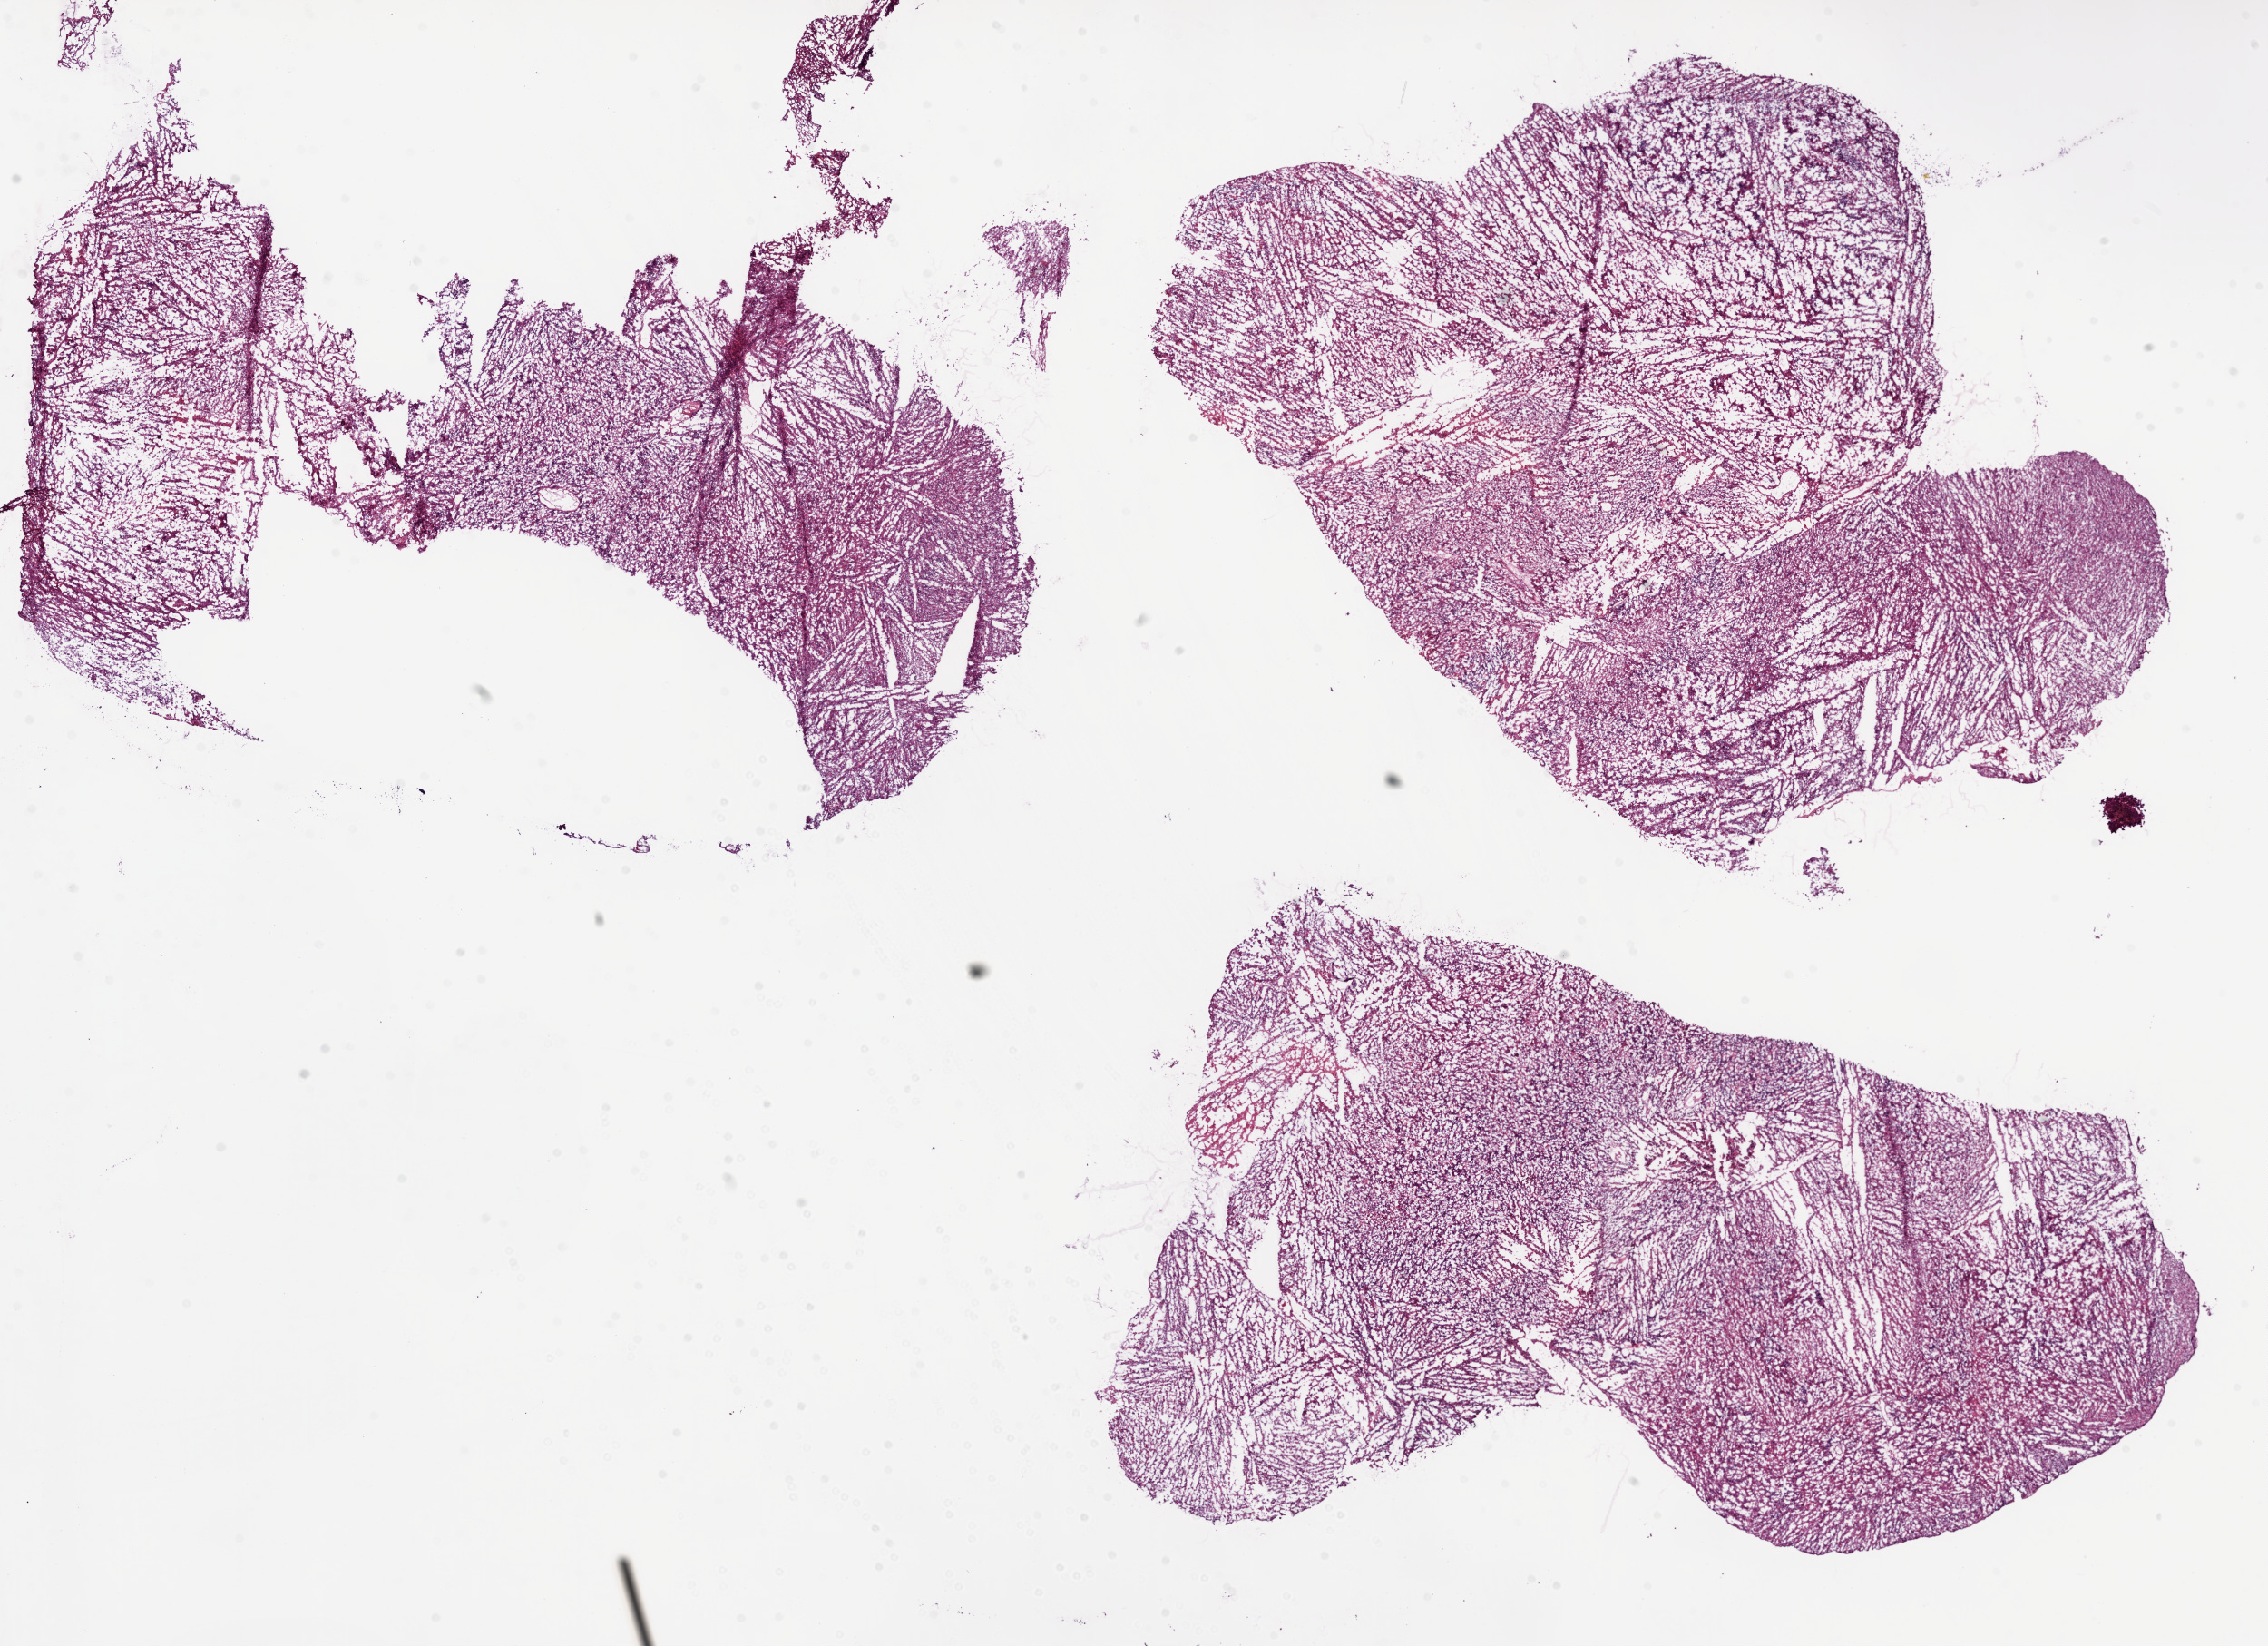
H&E whole-slide image — shown as a low-resolution overview of the whole scanned area (about 20.1 x 14.6 mm); frozen section; sample: primary tumour, brain. Female, age 76 years at initial diagnosis. Pathologist review of this section (percent, as recorded): tumour cells 80%, tumour nuclei 80%.
Pathologic diagnosis: Glioblastoma.